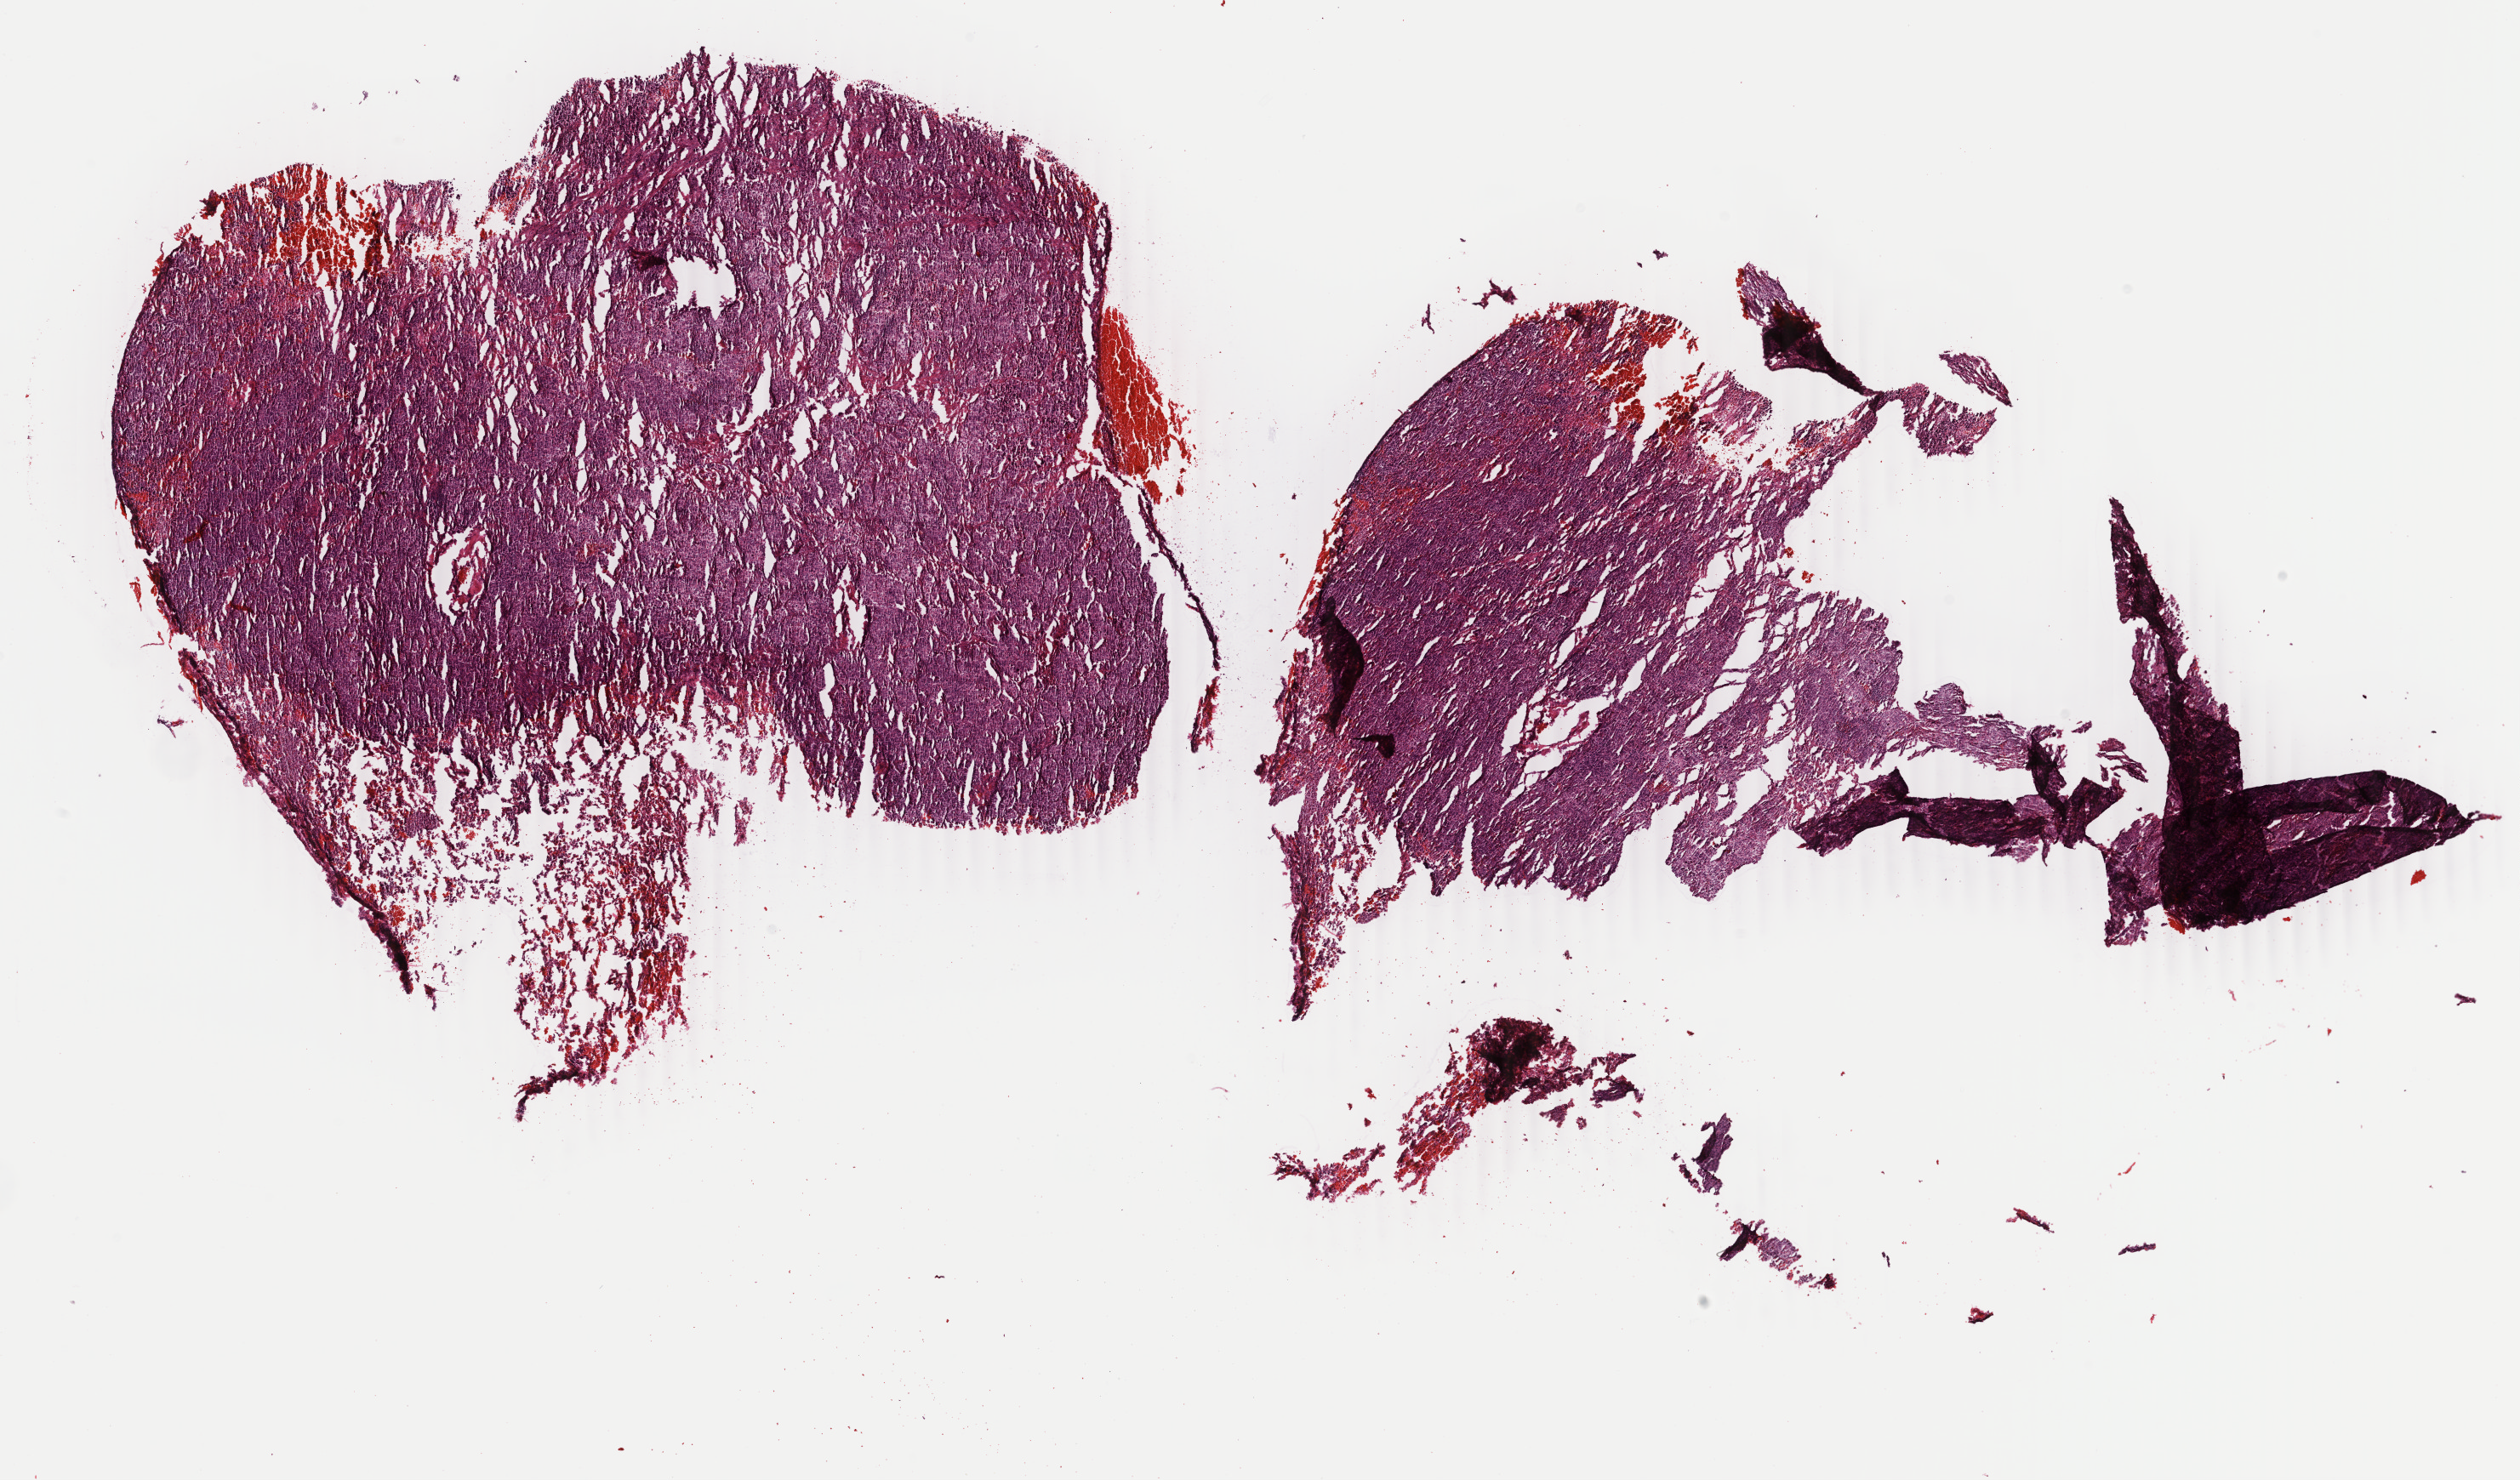
H&E whole-slide image, low-resolution overview of the scanned area, about 23.6 x 13.8 mm; frozen section from the bottom of the tissue portion; sample: primary tumour, lung. Patient: female, age at initial diagnosis 60 years. Slide review estimates, as recorded: tumour cells 70%, tumour nuclei 70%, normal cells 0%, stromal cells 21%, necrosis 9%. Infiltration values recorded for this section: lymphocyte infiltration 3%, monocyte infiltration 2%, neutrophil infiltration 3%.
Laterality: left. AJCC pathologic stage: IA (6th edition). TNM: T1 N0 M0. Pathologic diagnosis: Adenocarcinoma, NOS (upper lobe, lung).